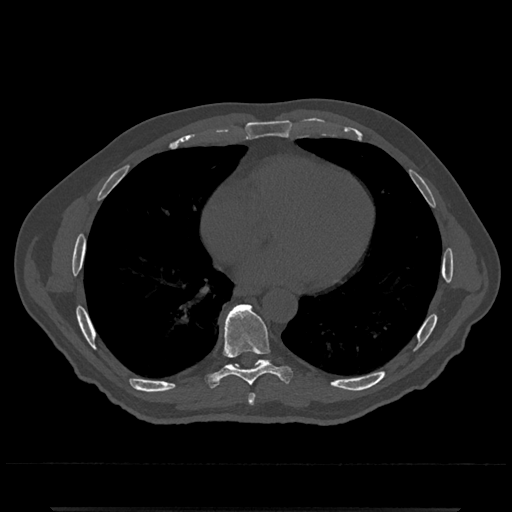
CT including the spine, one axial slice. Position 665 of 797 along the scan axis. Reconstruction kernel Br40s/3. 120 kVp. Bone window (W 1800 / L 400 HU). 512 × 512 image matrix, field of view 393 × 393 mm. Patient: male, 67 years. Case-level facts recorded for this patient, not image findings: primary cancer: prostate.
Structures marked on this image (semi-automatic segmentation, software-assisted and operator-edited):
- T7 vertebra: box from (x=248, y=394) to (x=255, y=404) px
- T8 vertebra: (x=206, y=304)–(x=293, y=386)
- T9 vertebra: (x=228, y=365)–(x=234, y=367)